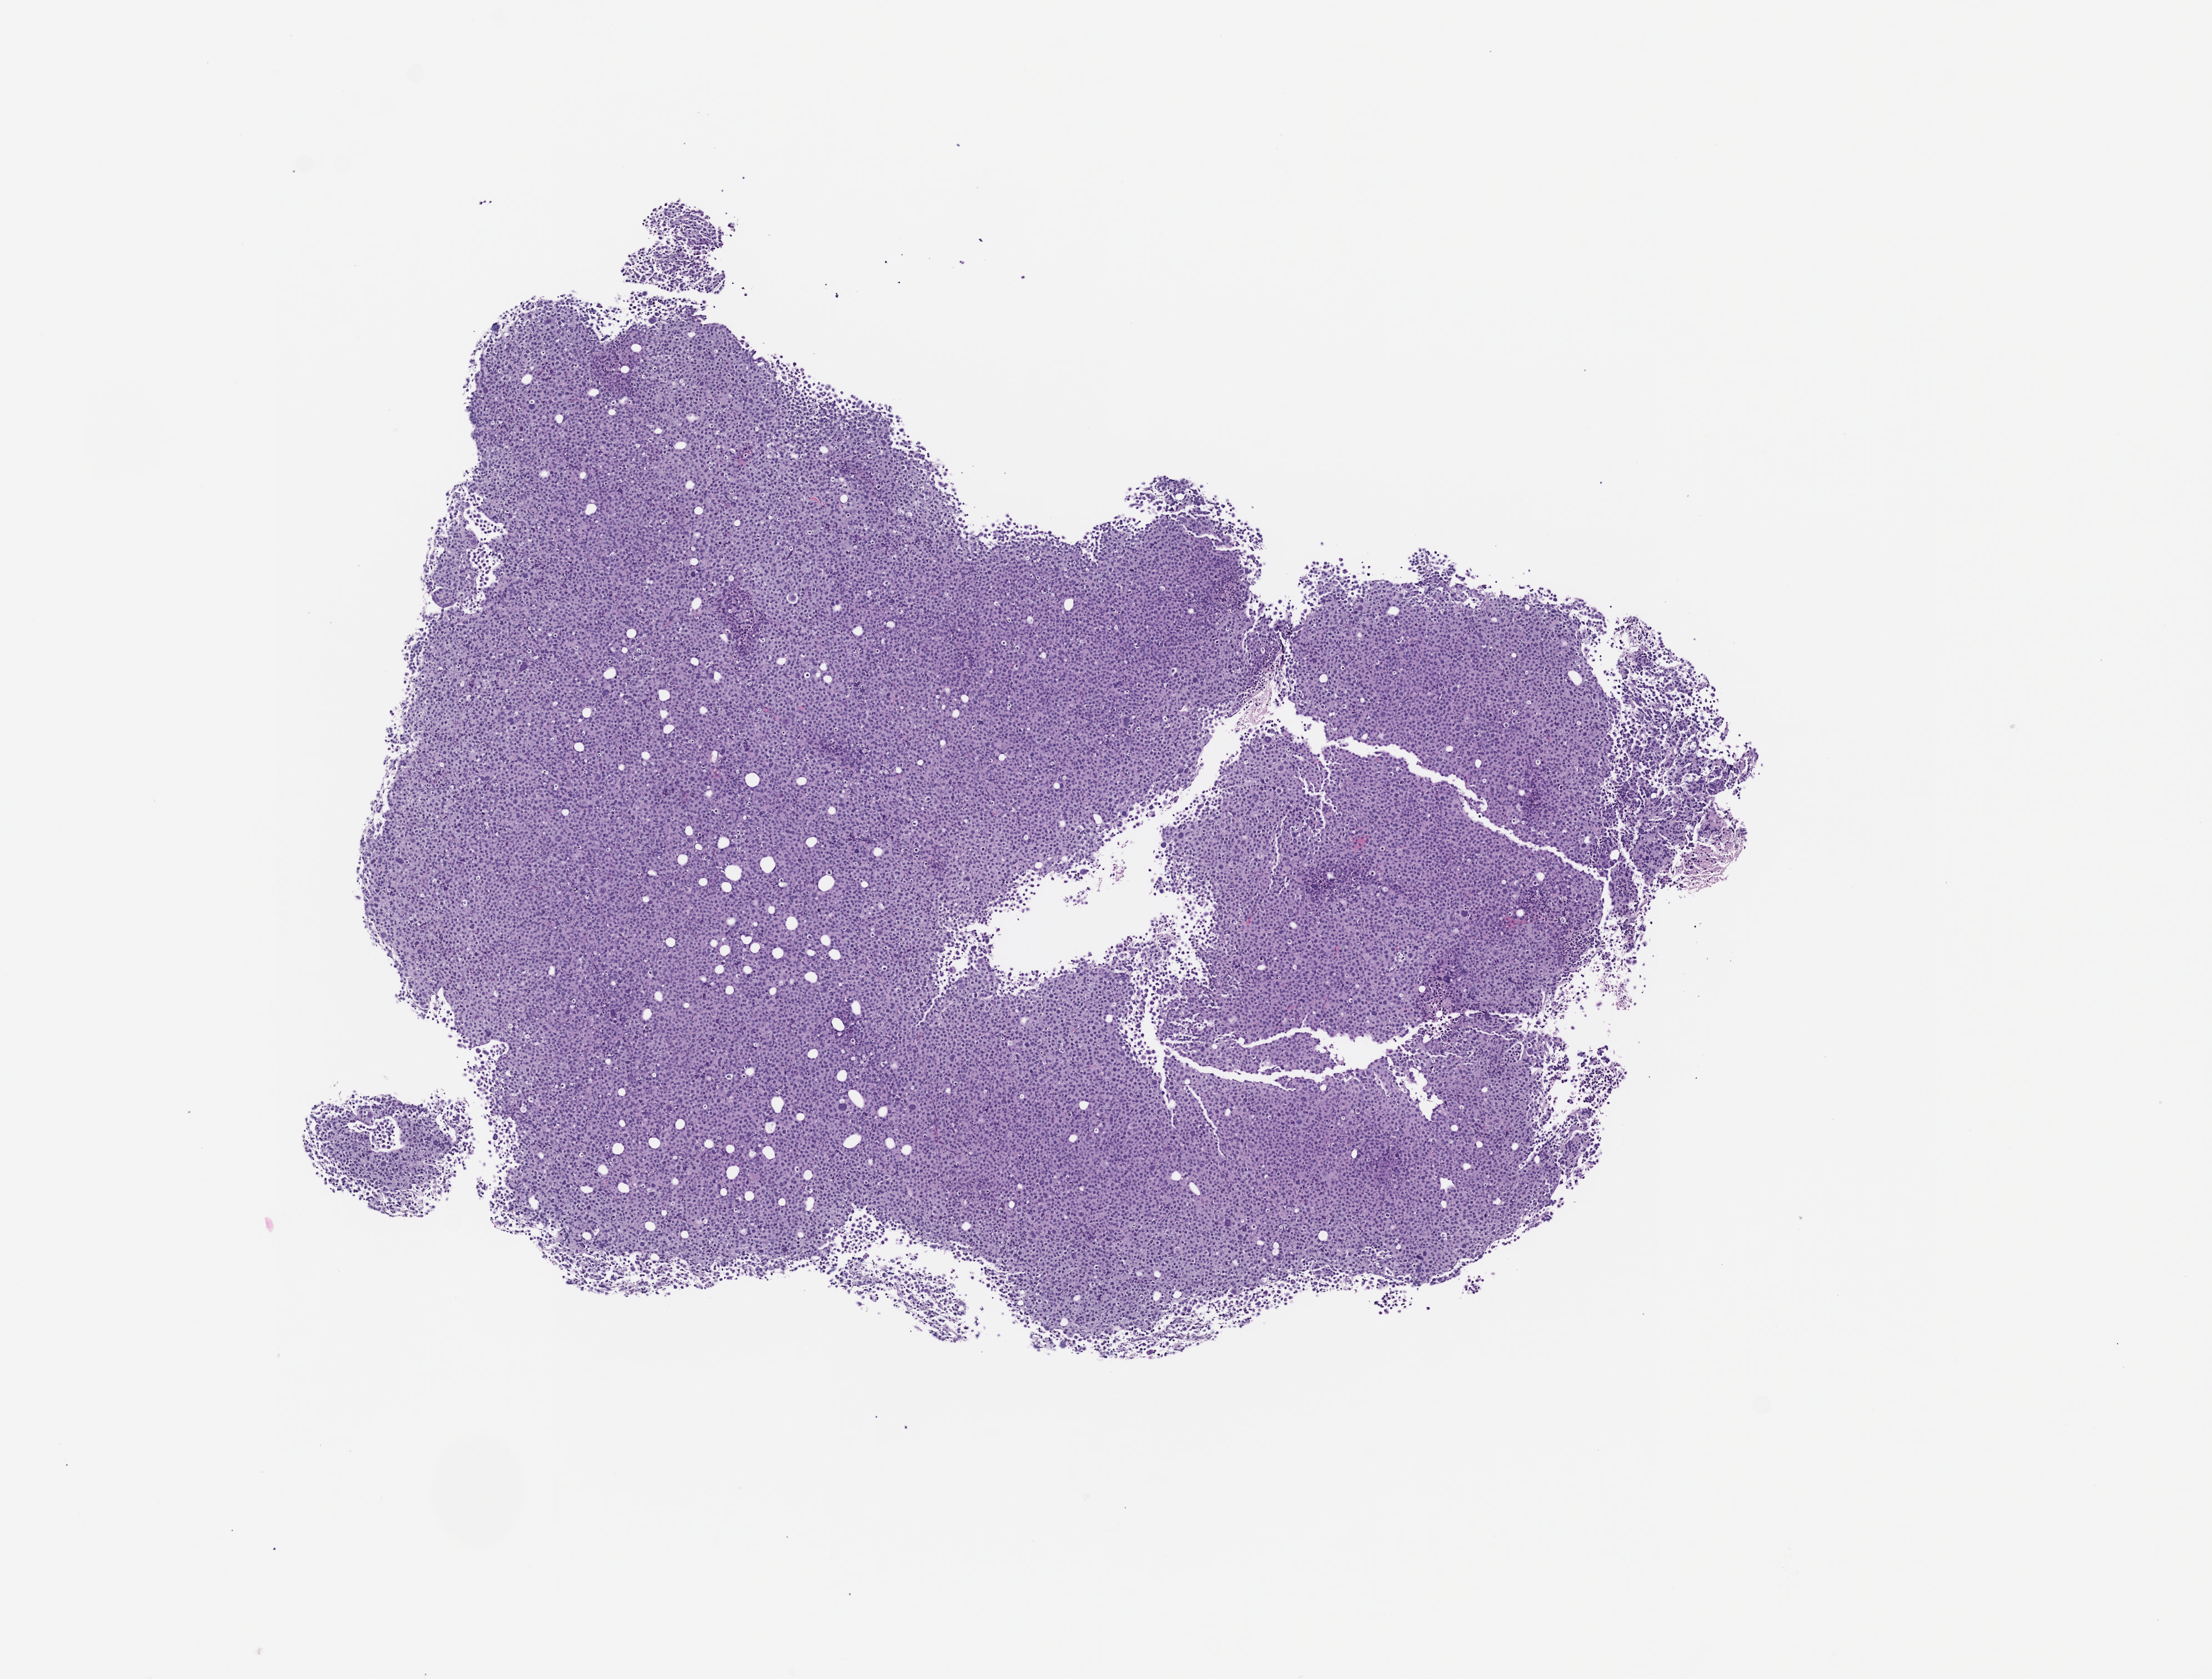
Whole-slide image, hematoxylin and eosin (H&E): patient-derived xenograft (human tumor grown in a mouse), passage 3 — a low-resolution overview of the entire scanned area, about 8.0 x 6.1 mm. Formalin-fixed, paraffin-embedded (FFPE) tissue. Originating tumor site category: bladder.
Originating patient diagnosis: Urothelial Carcinoma.